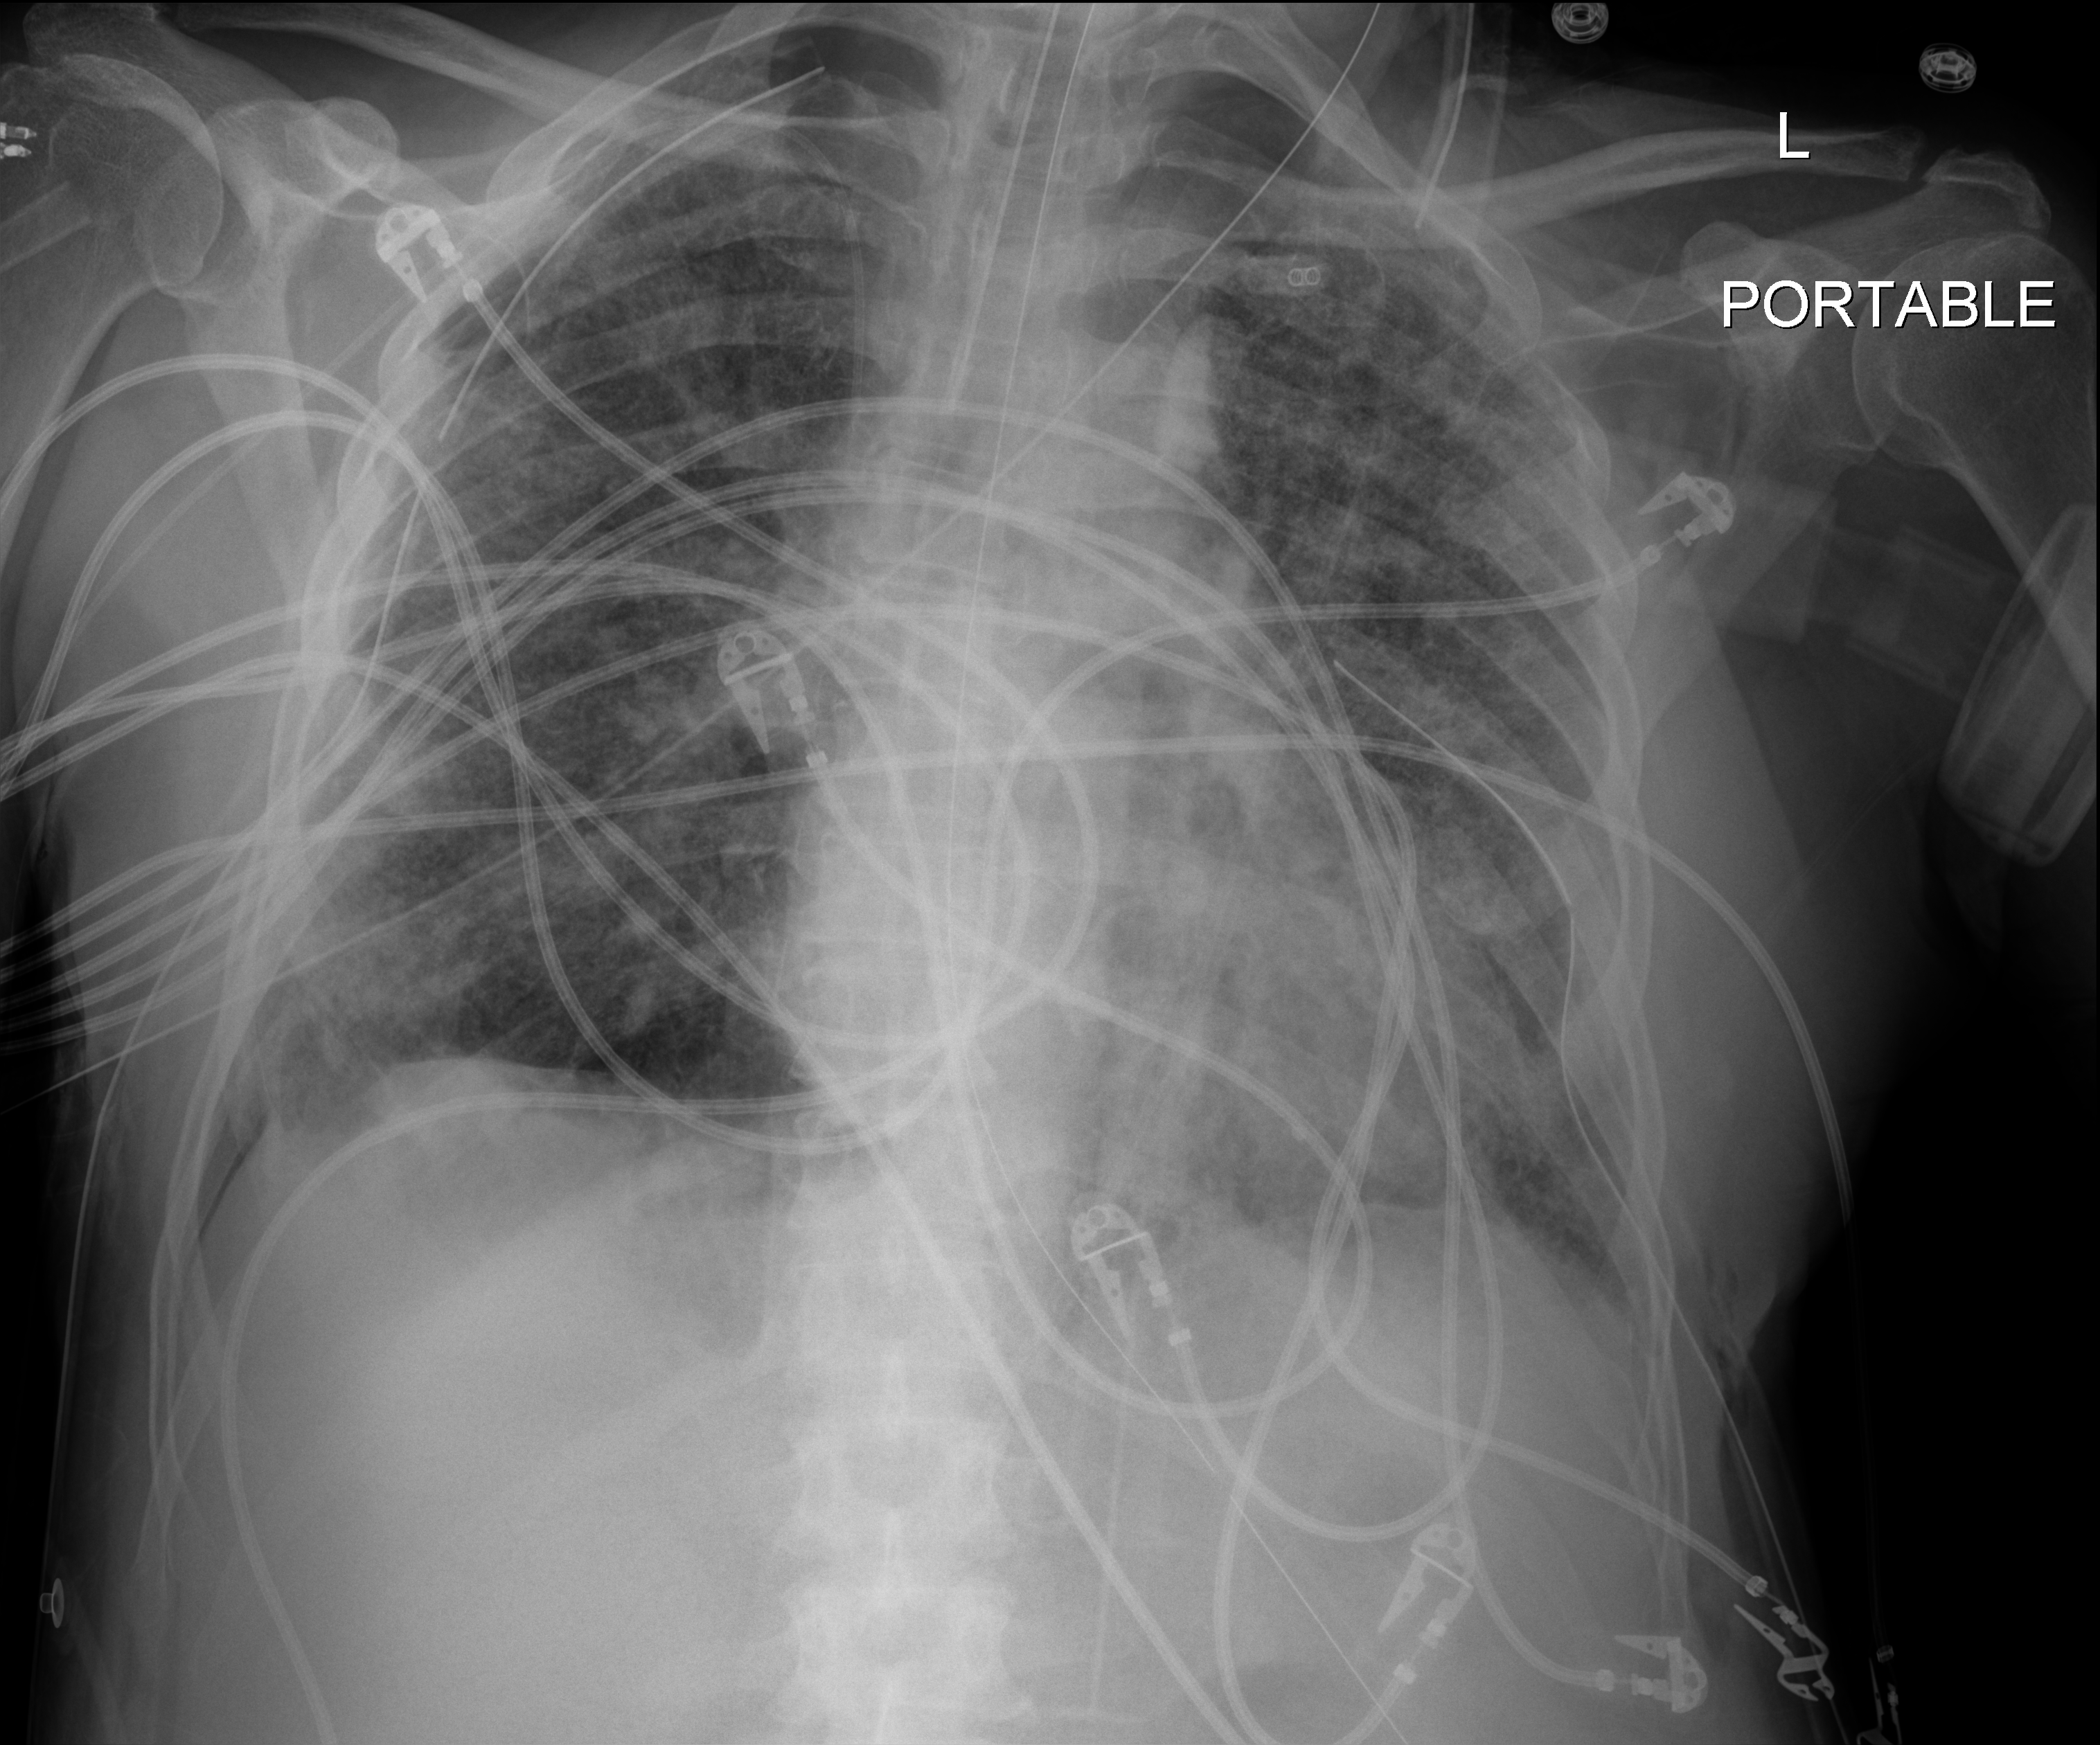
Bedside chest radiograph (digital radiography), anteroposterior (AP) projection. Patient hospitalised with COVID-19; male, aged 60–74 years.
From the hospital-stay record, not from the radiograph (when in the stay this image was taken is not recorded):
- admitted to intensive care during this hospital stay: yes
- mechanically ventilated during this hospital stay: yes
- other chronic lung disease (admission record): yes